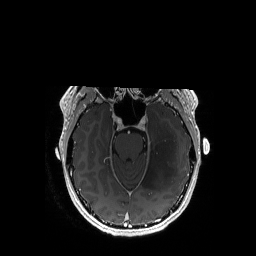
Brain MRI from a brain-tumour surgery series, one axial slice. Slice 116 of 192 in the series (ordered by position). T1-weighted post-contrast. 1 mm slice thickness. 256 × 256 image matrix, field of view 256 × 256 mm. Case-level facts recorded for this patient, not image findings: histopathology: Astrocytoma; WHO grade: 3; IDH mutation: yes.
Annotated regions visible in this slice (manually delineated by an expert):
- tumour: bounding box (x1, y1, x2, y2) in pixels: (142, 114, 178, 190)